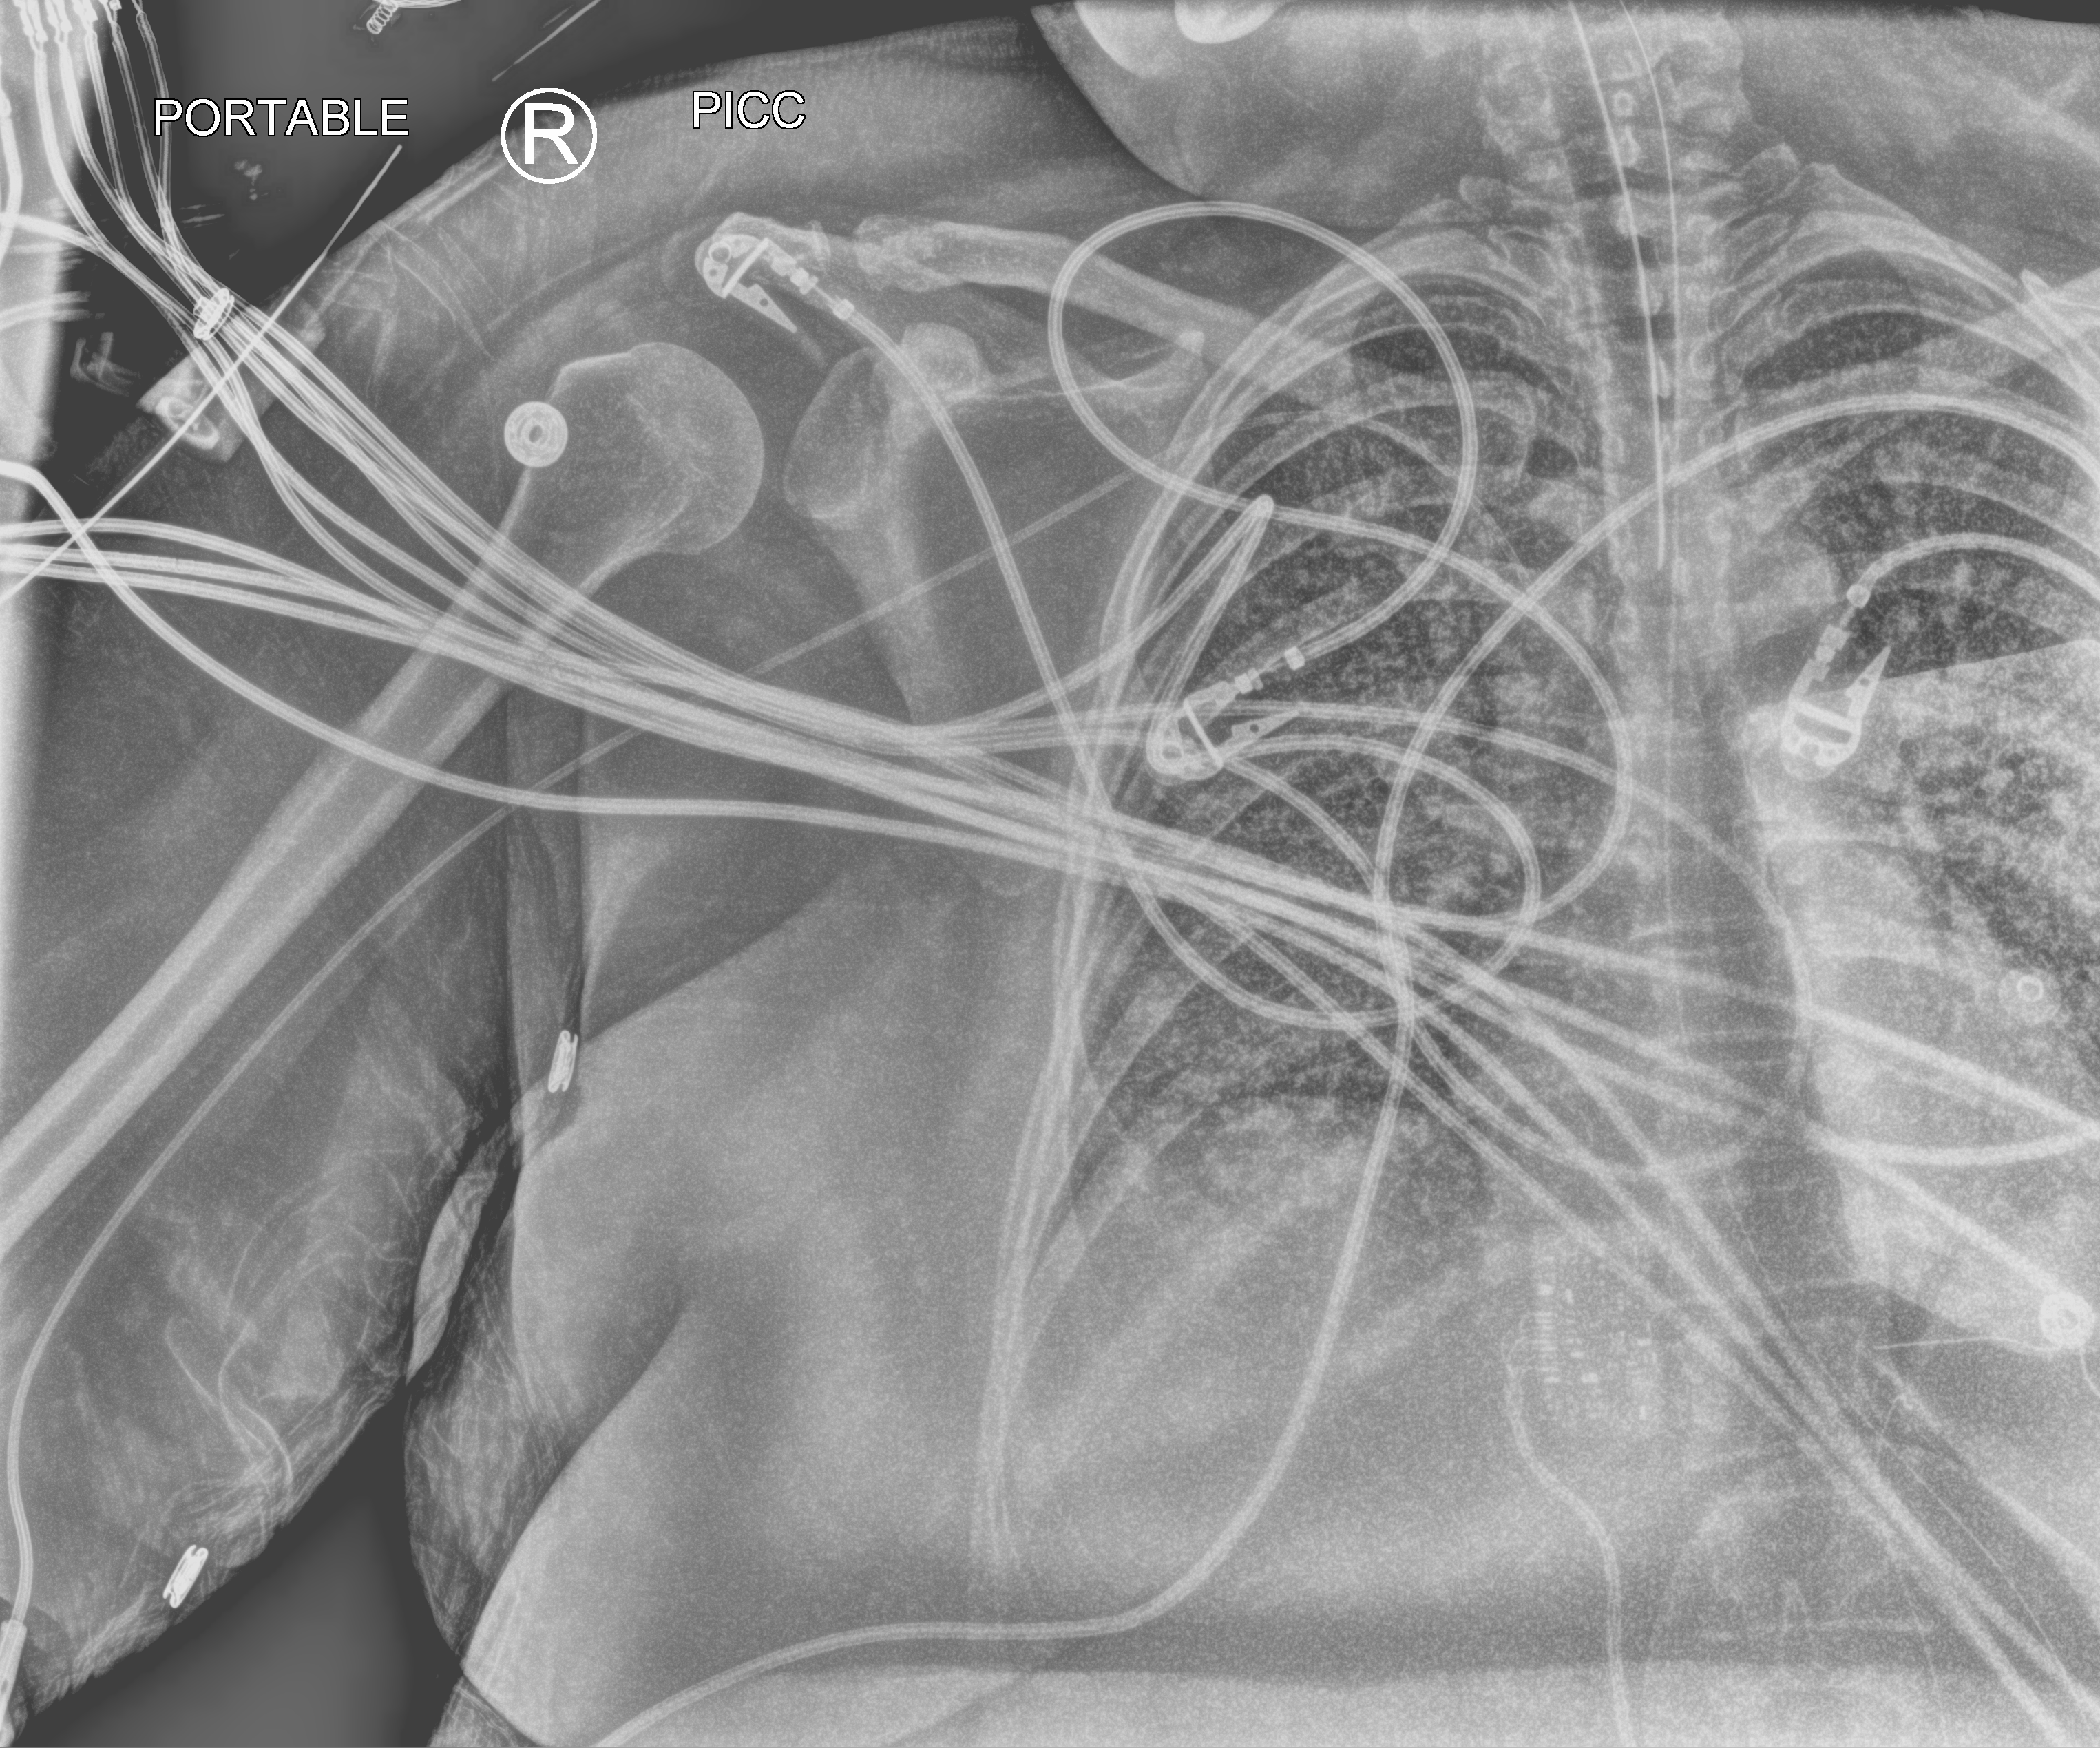
Bedside chest radiograph (computed radiography); anteroposterior (AP) projection. Patient hospitalised with COVID-19; female, aged 18–59 years.
Admission-level facts for this patient (not findings on this image; timing relative to this image not recorded): admitted to intensive care during this hospital stay: yes; mechanically ventilated during this hospital stay: yes.